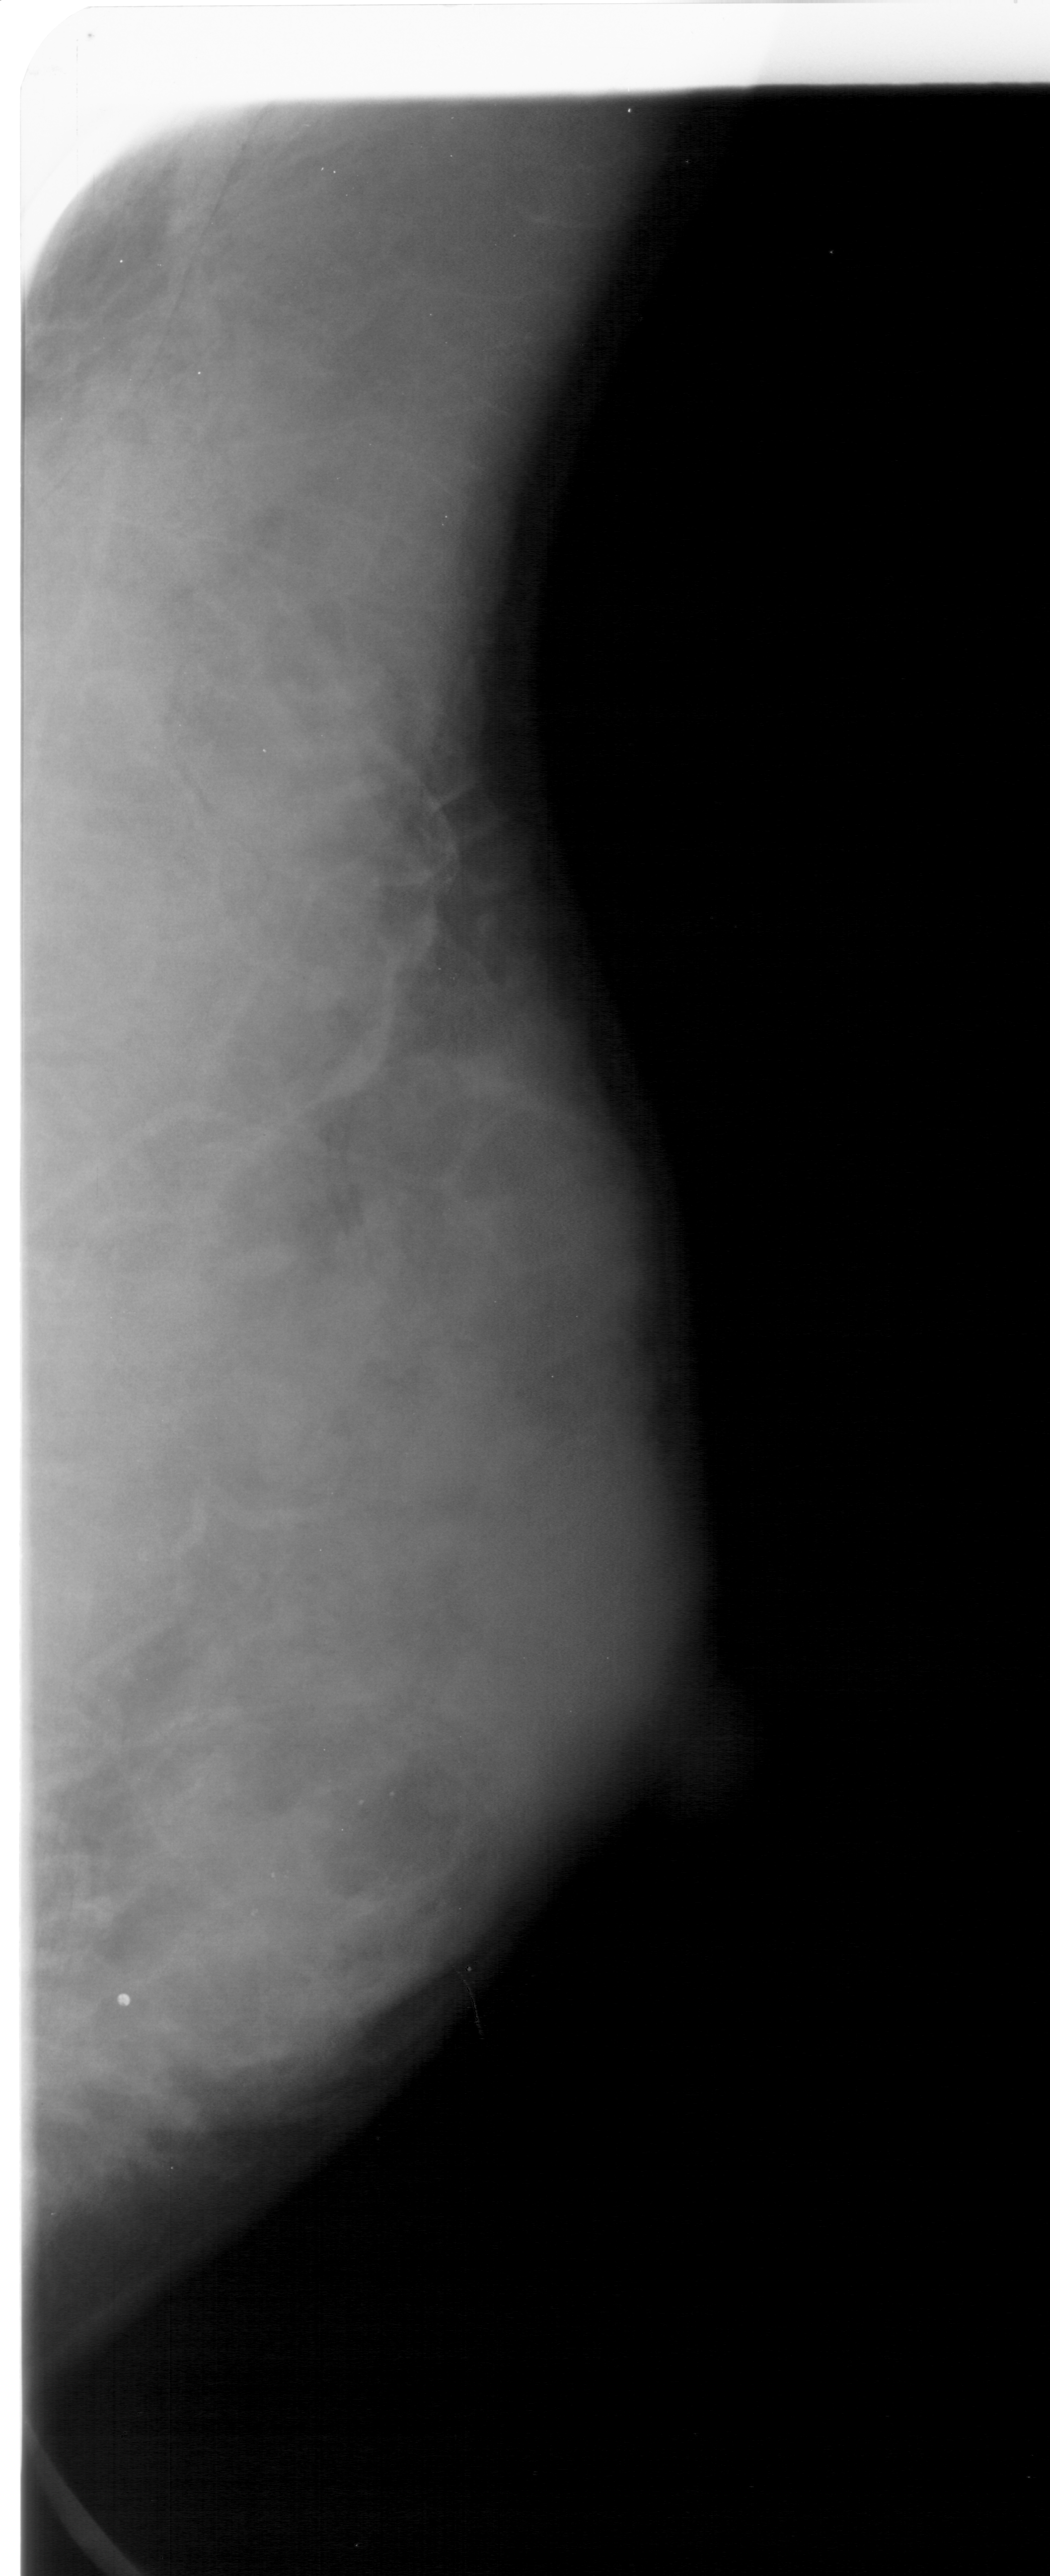
Digitized screen-film mammogram; right breast; MLO view; BI-RADS breast density category 4 (scale 1–4).
- Radiologist-marked abnormalities on this image: calcifications, morphology pleomorphic, distribution segmental; BI-RADS assessment category 4; subtlety rating 3 on a 1 (subtle) to 5 (obvious) scale; pathology (as recorded): benign.